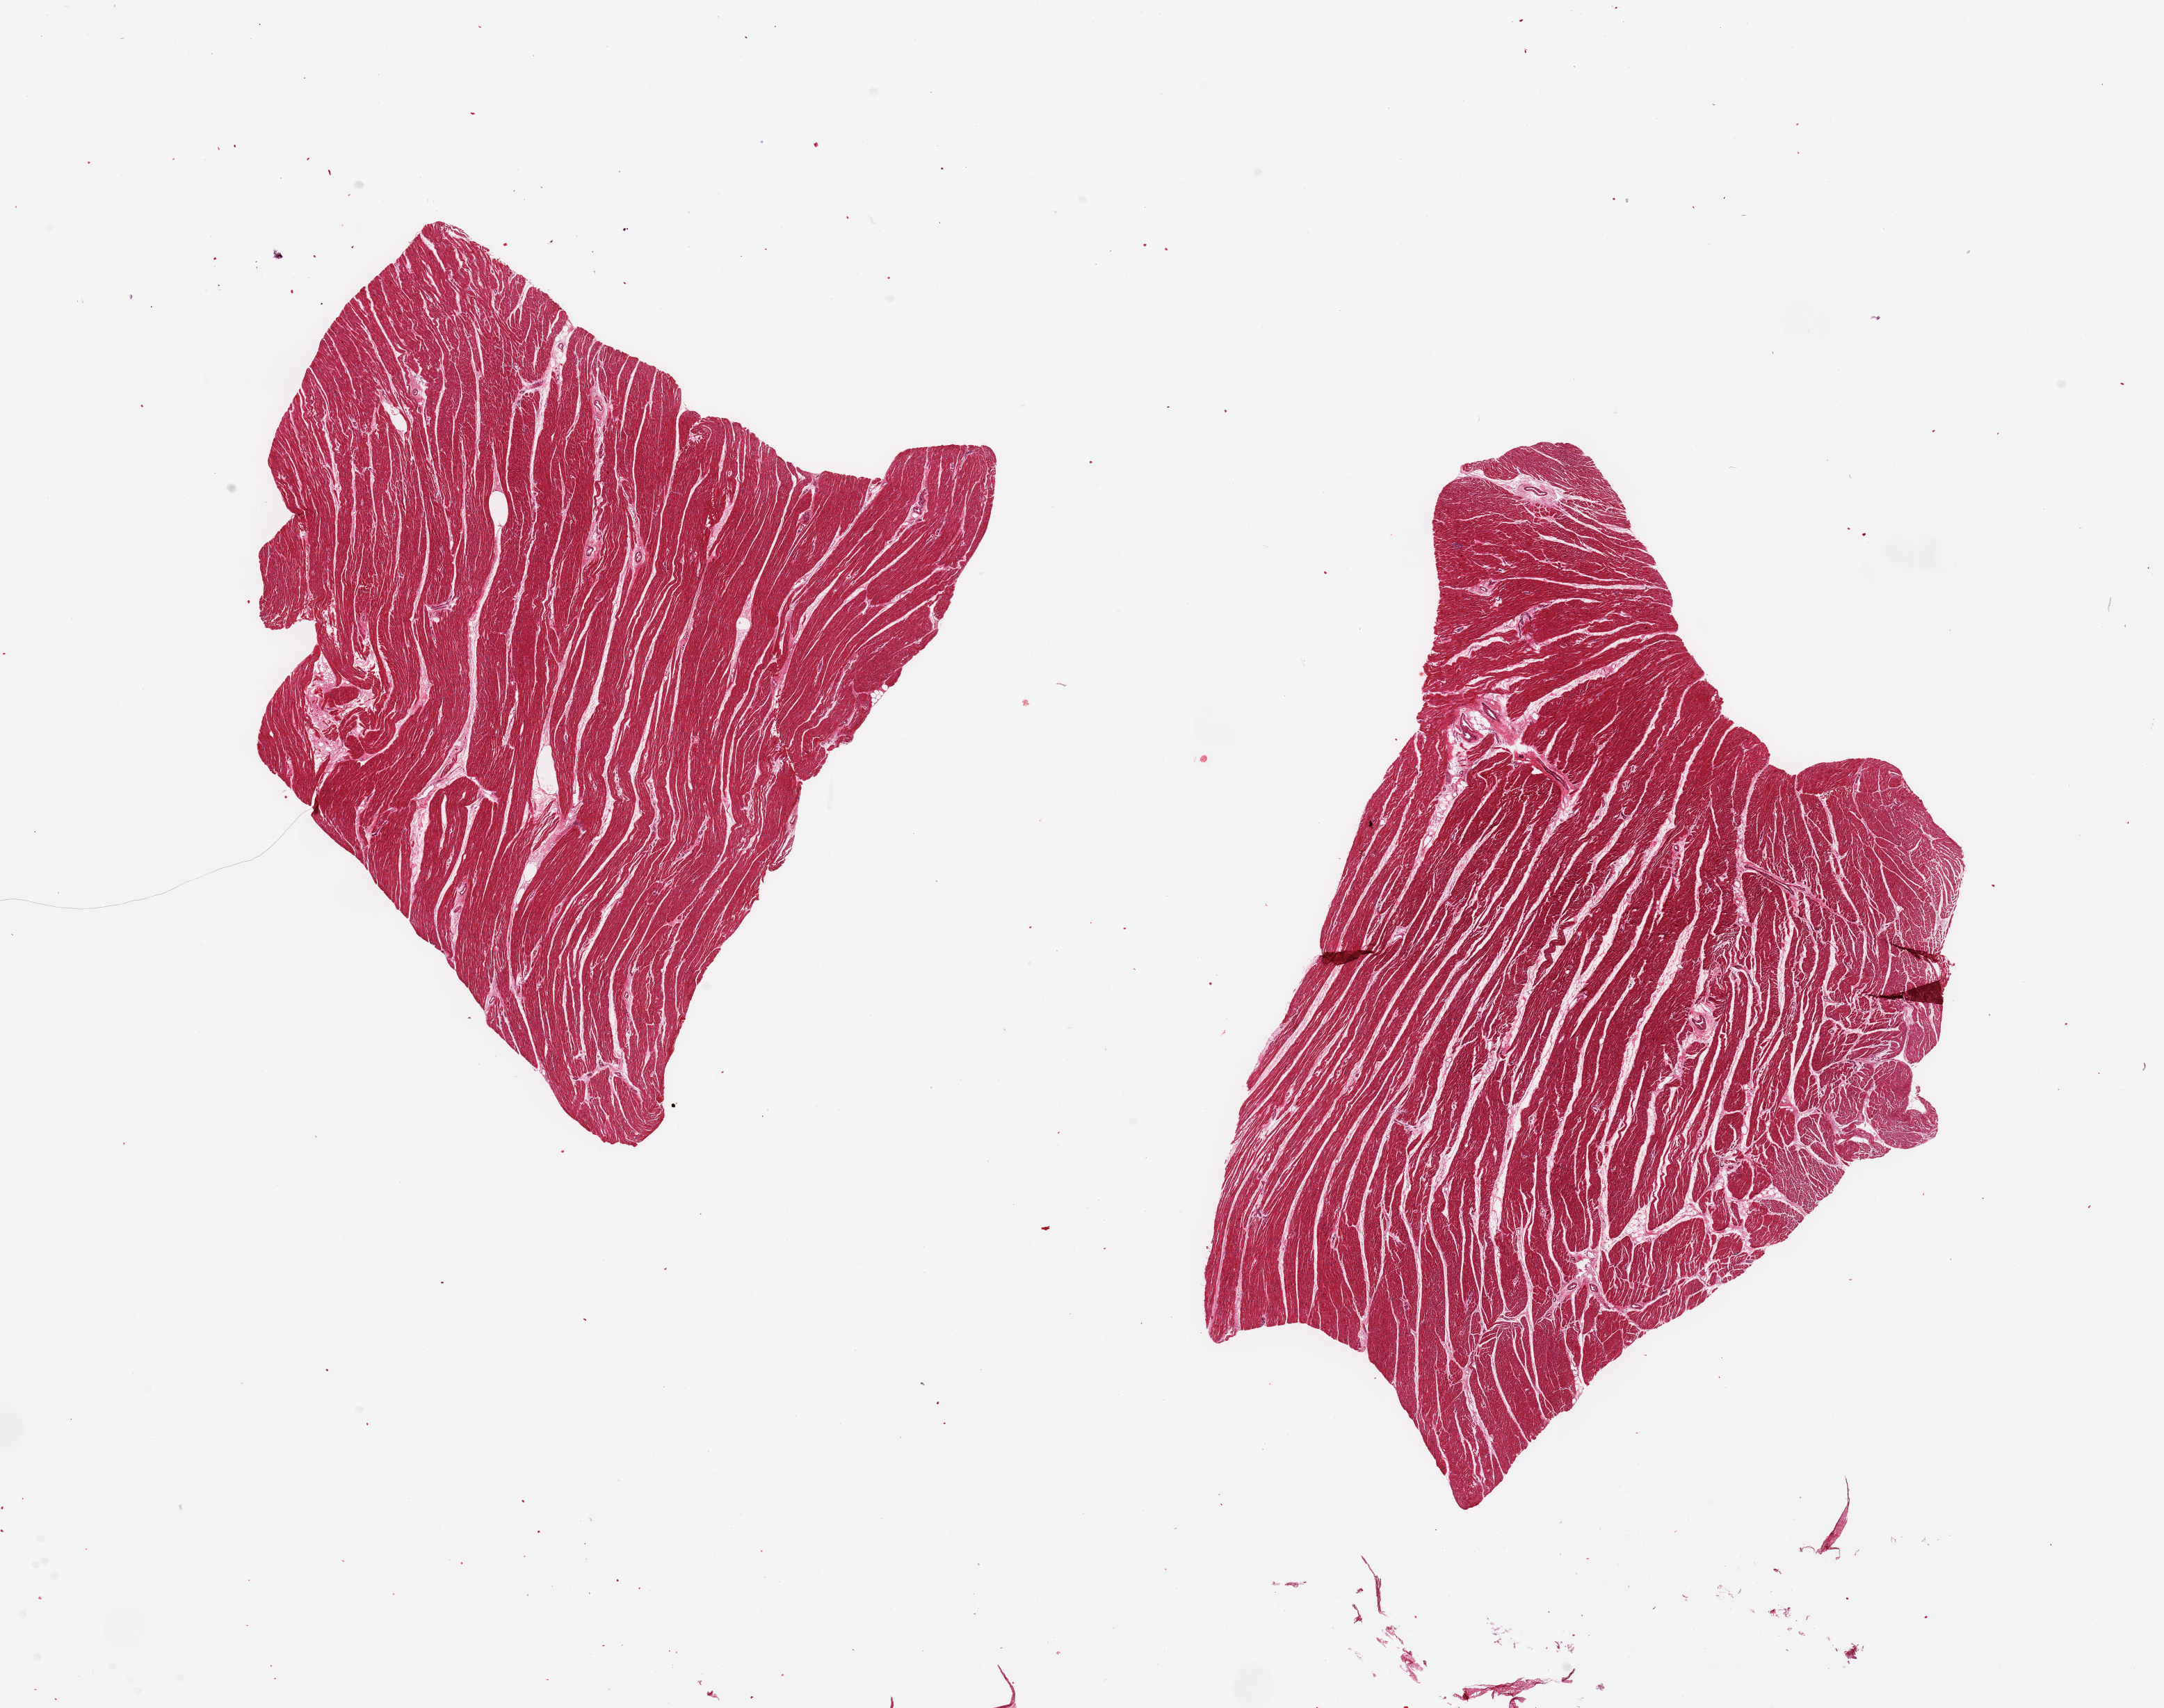
Digitized haematoxylin and eosin-stained section — a low-resolution overview of the entire scanned area, about 24.6 x 19.4 mm (from a 20x scan); PAXgene-fixed paraffin-embedded (PFPE) section; section of heart (target tissue); tissue donor sample. Male donor.
Pathologist's review note for this sample: 2 pieces.